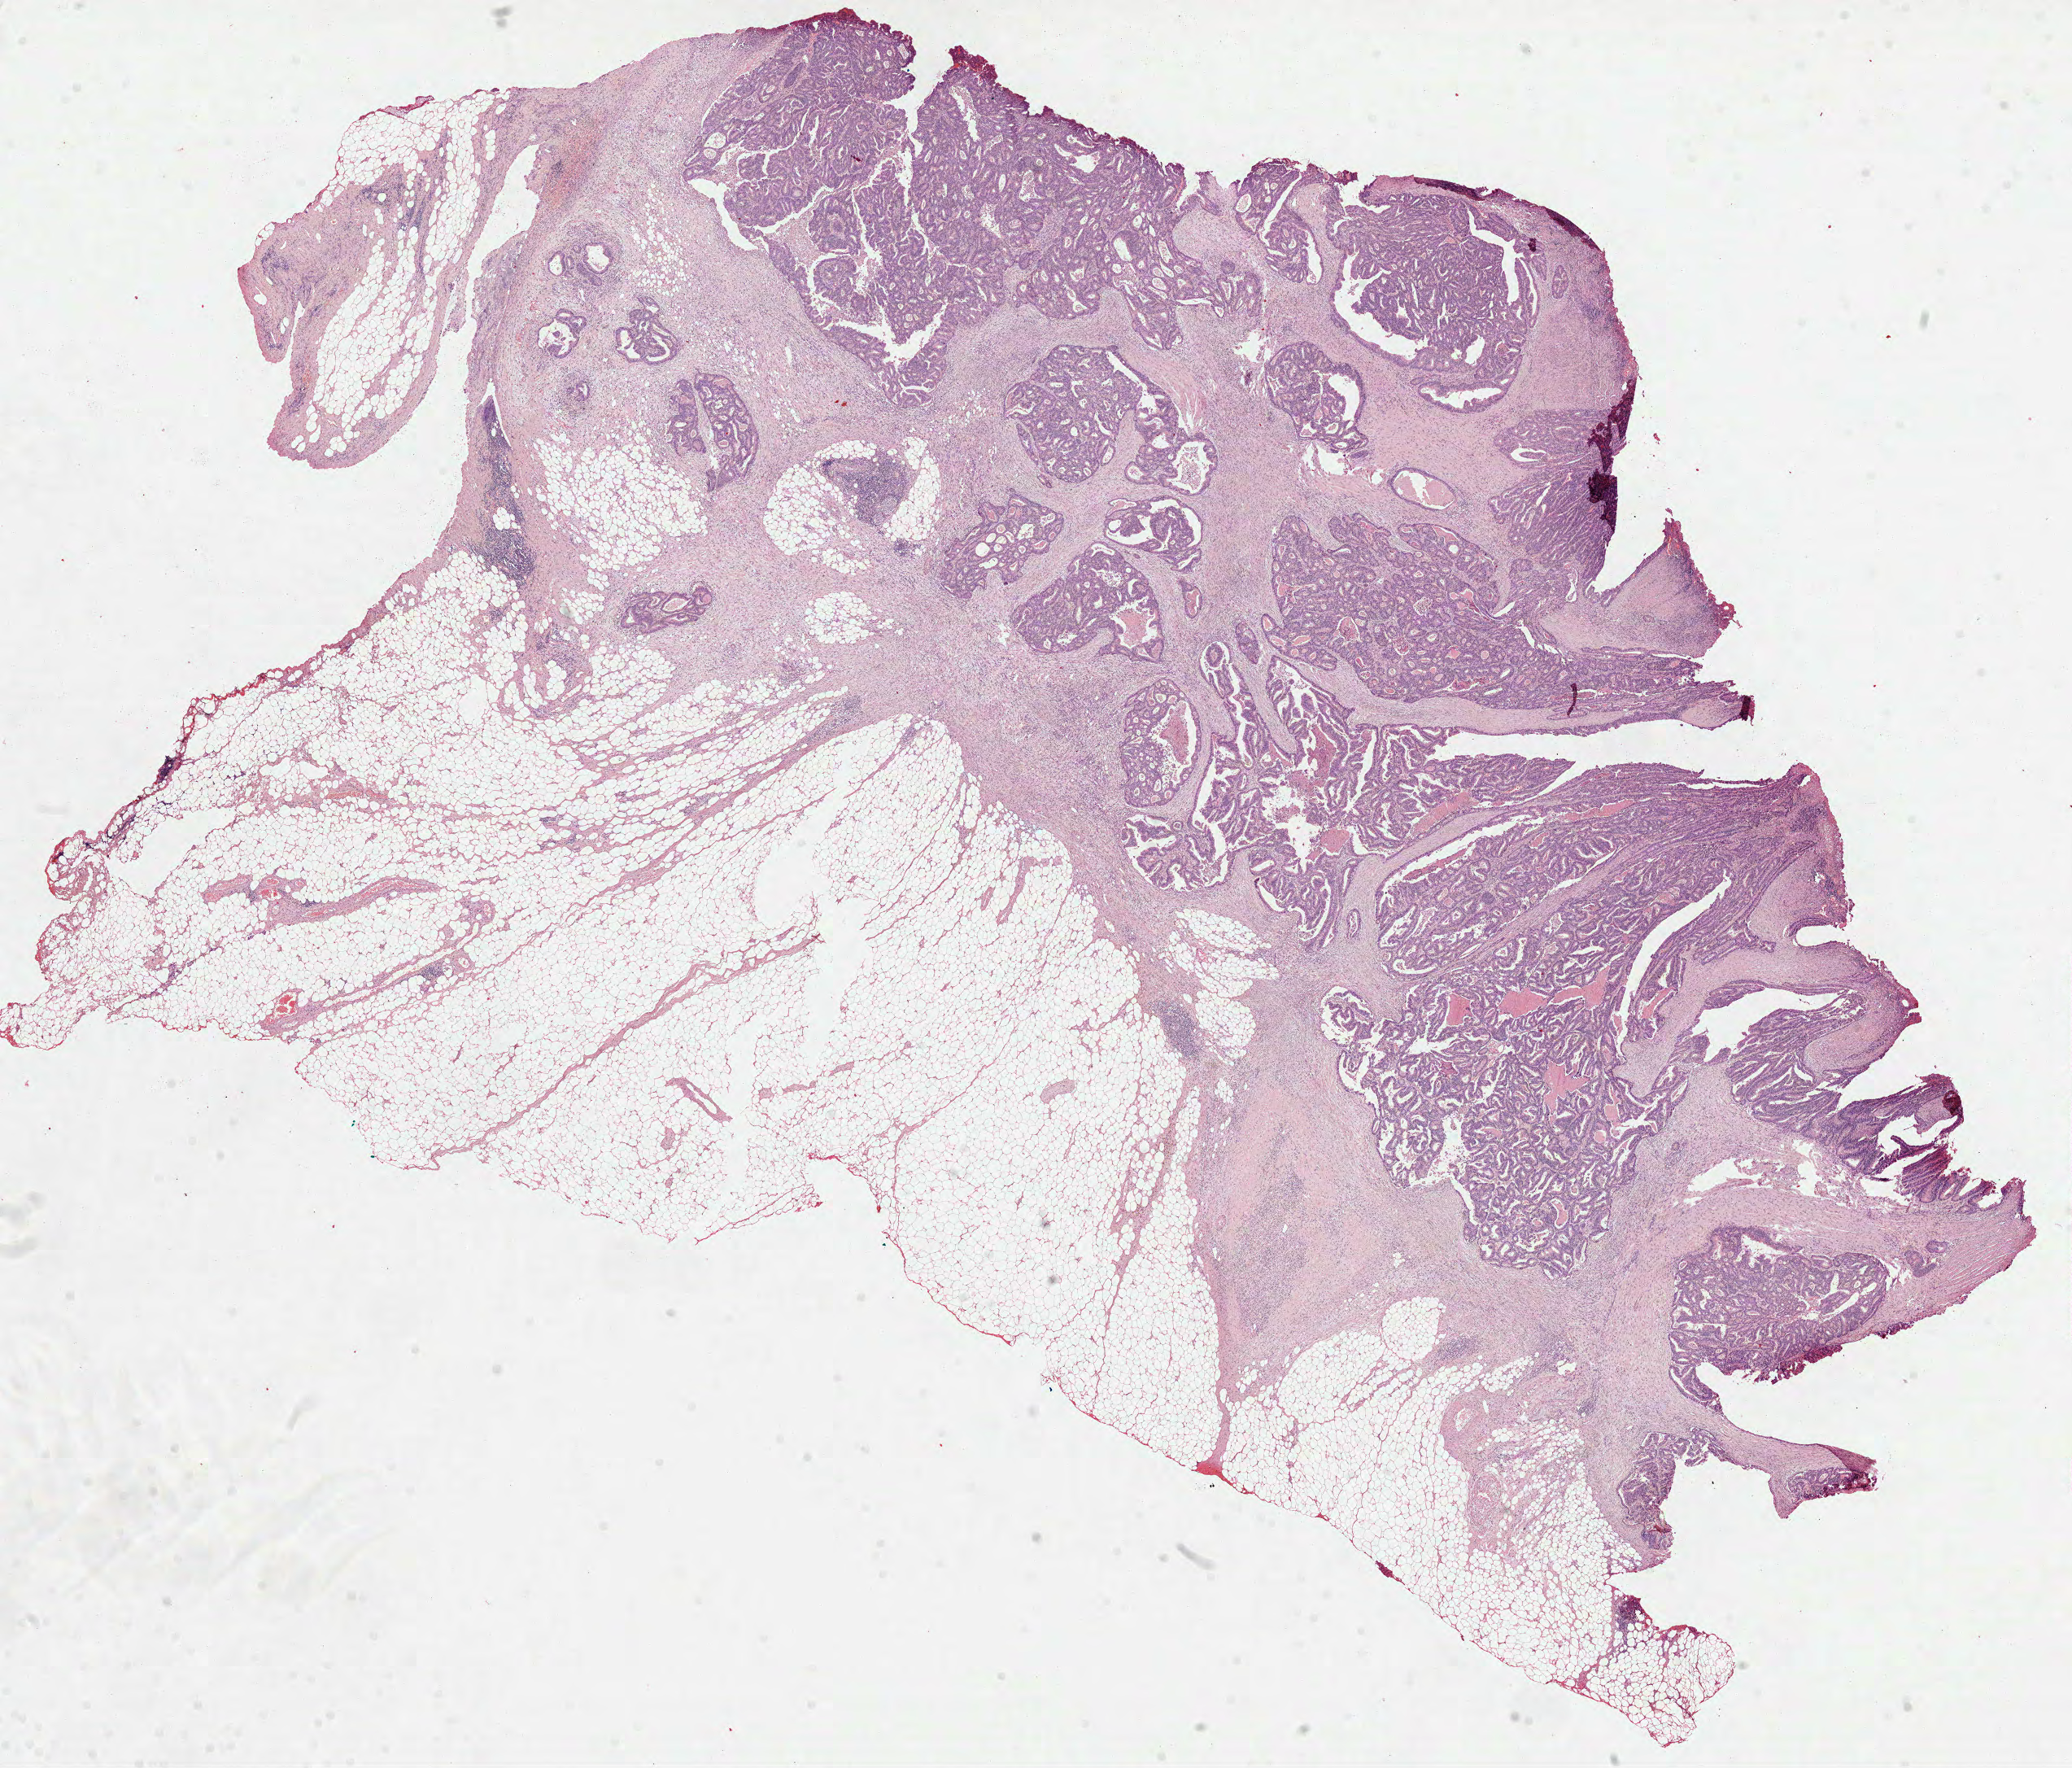
H&E-stained whole-slide image — low-resolution overview of the scanned area, about 20.5 x 17.5 mm (slide scanned at 40x). Formalin-fixed paraffin-embedded (FFPE) diagnostic section. Sample: primary tumour, rectum. Patient: male, age at initial diagnosis 63 years.
TNM: T3 N0 M0. AJCC pathologic stage: IIC (7th edition). Lymph nodes positive (case pathology): 0 of 16 examined. Histologic diagnosis: Tubular adenocarcinoma.